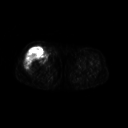
FDG PET of an extremity soft-tissue mass (from a PET/CT study), one axial slice. Slice 236 of 311 in the series (ordered by position). 128 × 128 image matrix, field of view 500 × 500 mm. Female patient, age 57 years. From the clinical record (not read from this slice): histological type: pleiomorphic undifferentiated sarcoma; grade: high; site of the primary tumour: right quadricep.
Outlined on this slice (expert contour drawn on MRI and transferred to this co-registered scan by the dataset authors):
- tumour plus oedema (research contour): bounding box [x1, y1, x2, y2] px = [25, 48, 46, 70]
- tumour (research contour): [25, 48, 46, 70]